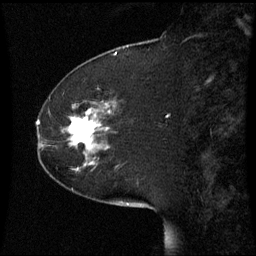
Breast MRI (dynamic contrast-enhanced), one sagittal slice; slice 18 of 60 in the series (ordered by position); dynamic contrast-enhanced series, image 2 of 3 at this slice position (ordered by acquisition); 1.5 T; TE 4.2 ms, TR 8.9 ms; 2.2 mm slice thickness; 256 × 256 image matrix, field of view 220 × 220 mm. Patient: female, 51 years. From the clinical record (not read from this slice): setting: breast cancer imaged before/during neoadjuvant chemotherapy; receptor status: HR-positive, HER2-negative.
Annotated regions visible in this slice (semi-automatic segmentation, software-assisted and operator-edited):
- analysis volume of interest (the breast-tissue region the enhancement analysis was run in; not a lesion): bounding box <44,102,109,169> (left, top, right, bottom; pixels)
- tumour enhancement mask (voxels above the 70 % enhancement threshold inside the analysis volume of interest): <70,118,99,145>